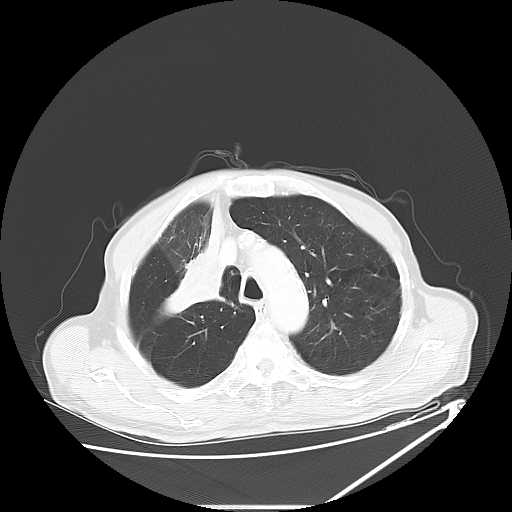
Chest CT, one axial slice. Position 47 of 60 along the scan axis. 120 kVp. Lung window (W 1500 / L -600 HU). 5 mm slice thickness. 512 × 512 image matrix, field of view 410 × 410 mm. Male patient, age 73 years. From the clinical record (not read from this slice): clinical TNM (as recorded): T2a N1 M0.
Structures marked on this image (bounding box drawn by a radiologist):
- lung tumour (recorded histology: squamous cell carcinoma): bounding box <165,200,247,327> (left, top, right, bottom; pixels)